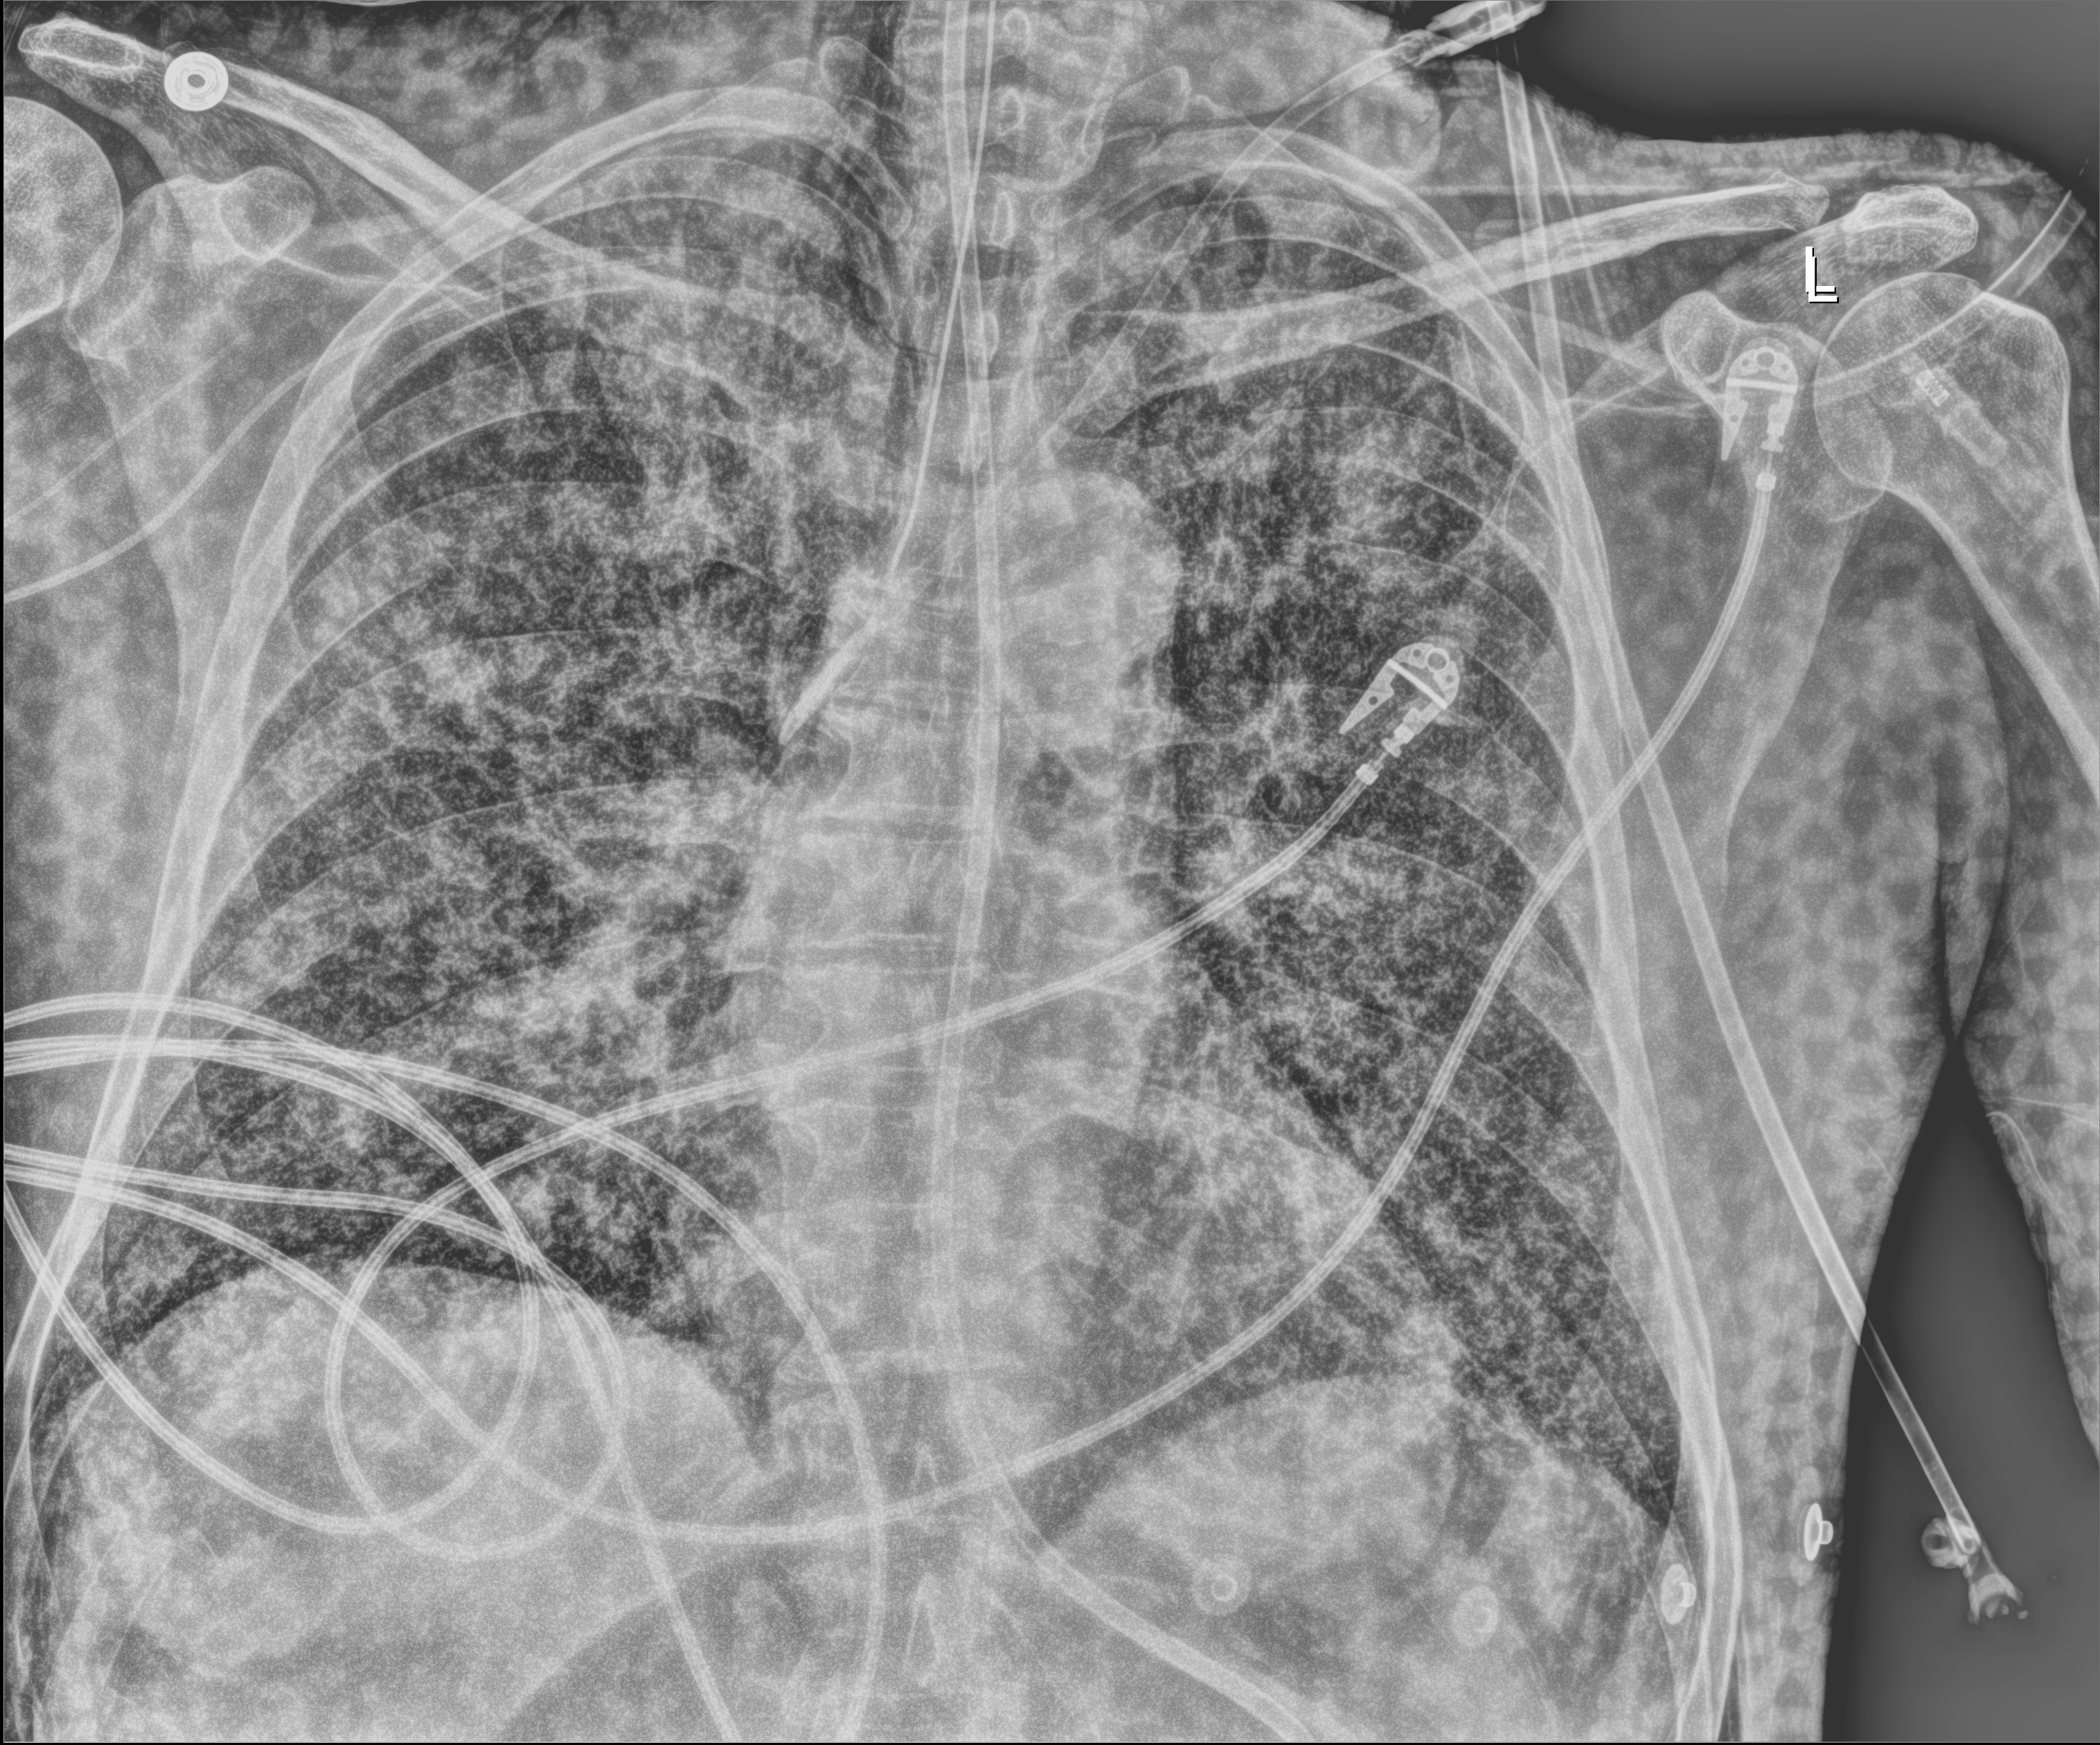
Chest X-ray (portable); anteroposterior (AP) projection. Patient hospitalised with COVID-19; male, aged 18–59 years.
Admission-level facts for this patient (not findings on this image; timing relative to this image not recorded): admitted to intensive care during this hospital stay: yes.